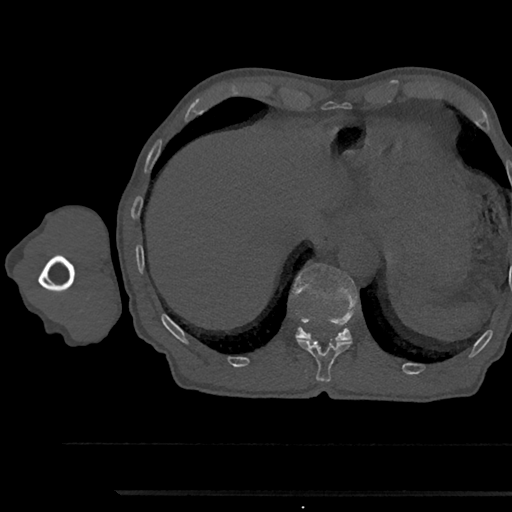
CT including the spine, one axial slice; slice 755 of 797 in the series (ordered by position); reconstruction kernel Br40s/3; 120 kVp; bone window (W 1800 / L 400 HU); 0.5 mm slice thickness; 512 × 512 image matrix, field of view 367 × 367 mm. Patient: male, 79 years. From the clinical record (not read from this slice): primary cancer: prostate.
Structures marked on this image (semi-automatic segmentation, software-assisted and operator-edited):
- T11 vertebra: bounding box [x1, y1, x2, y2] px = [297, 339, 351, 382]
- T12 vertebra: [291, 264, 358, 342]